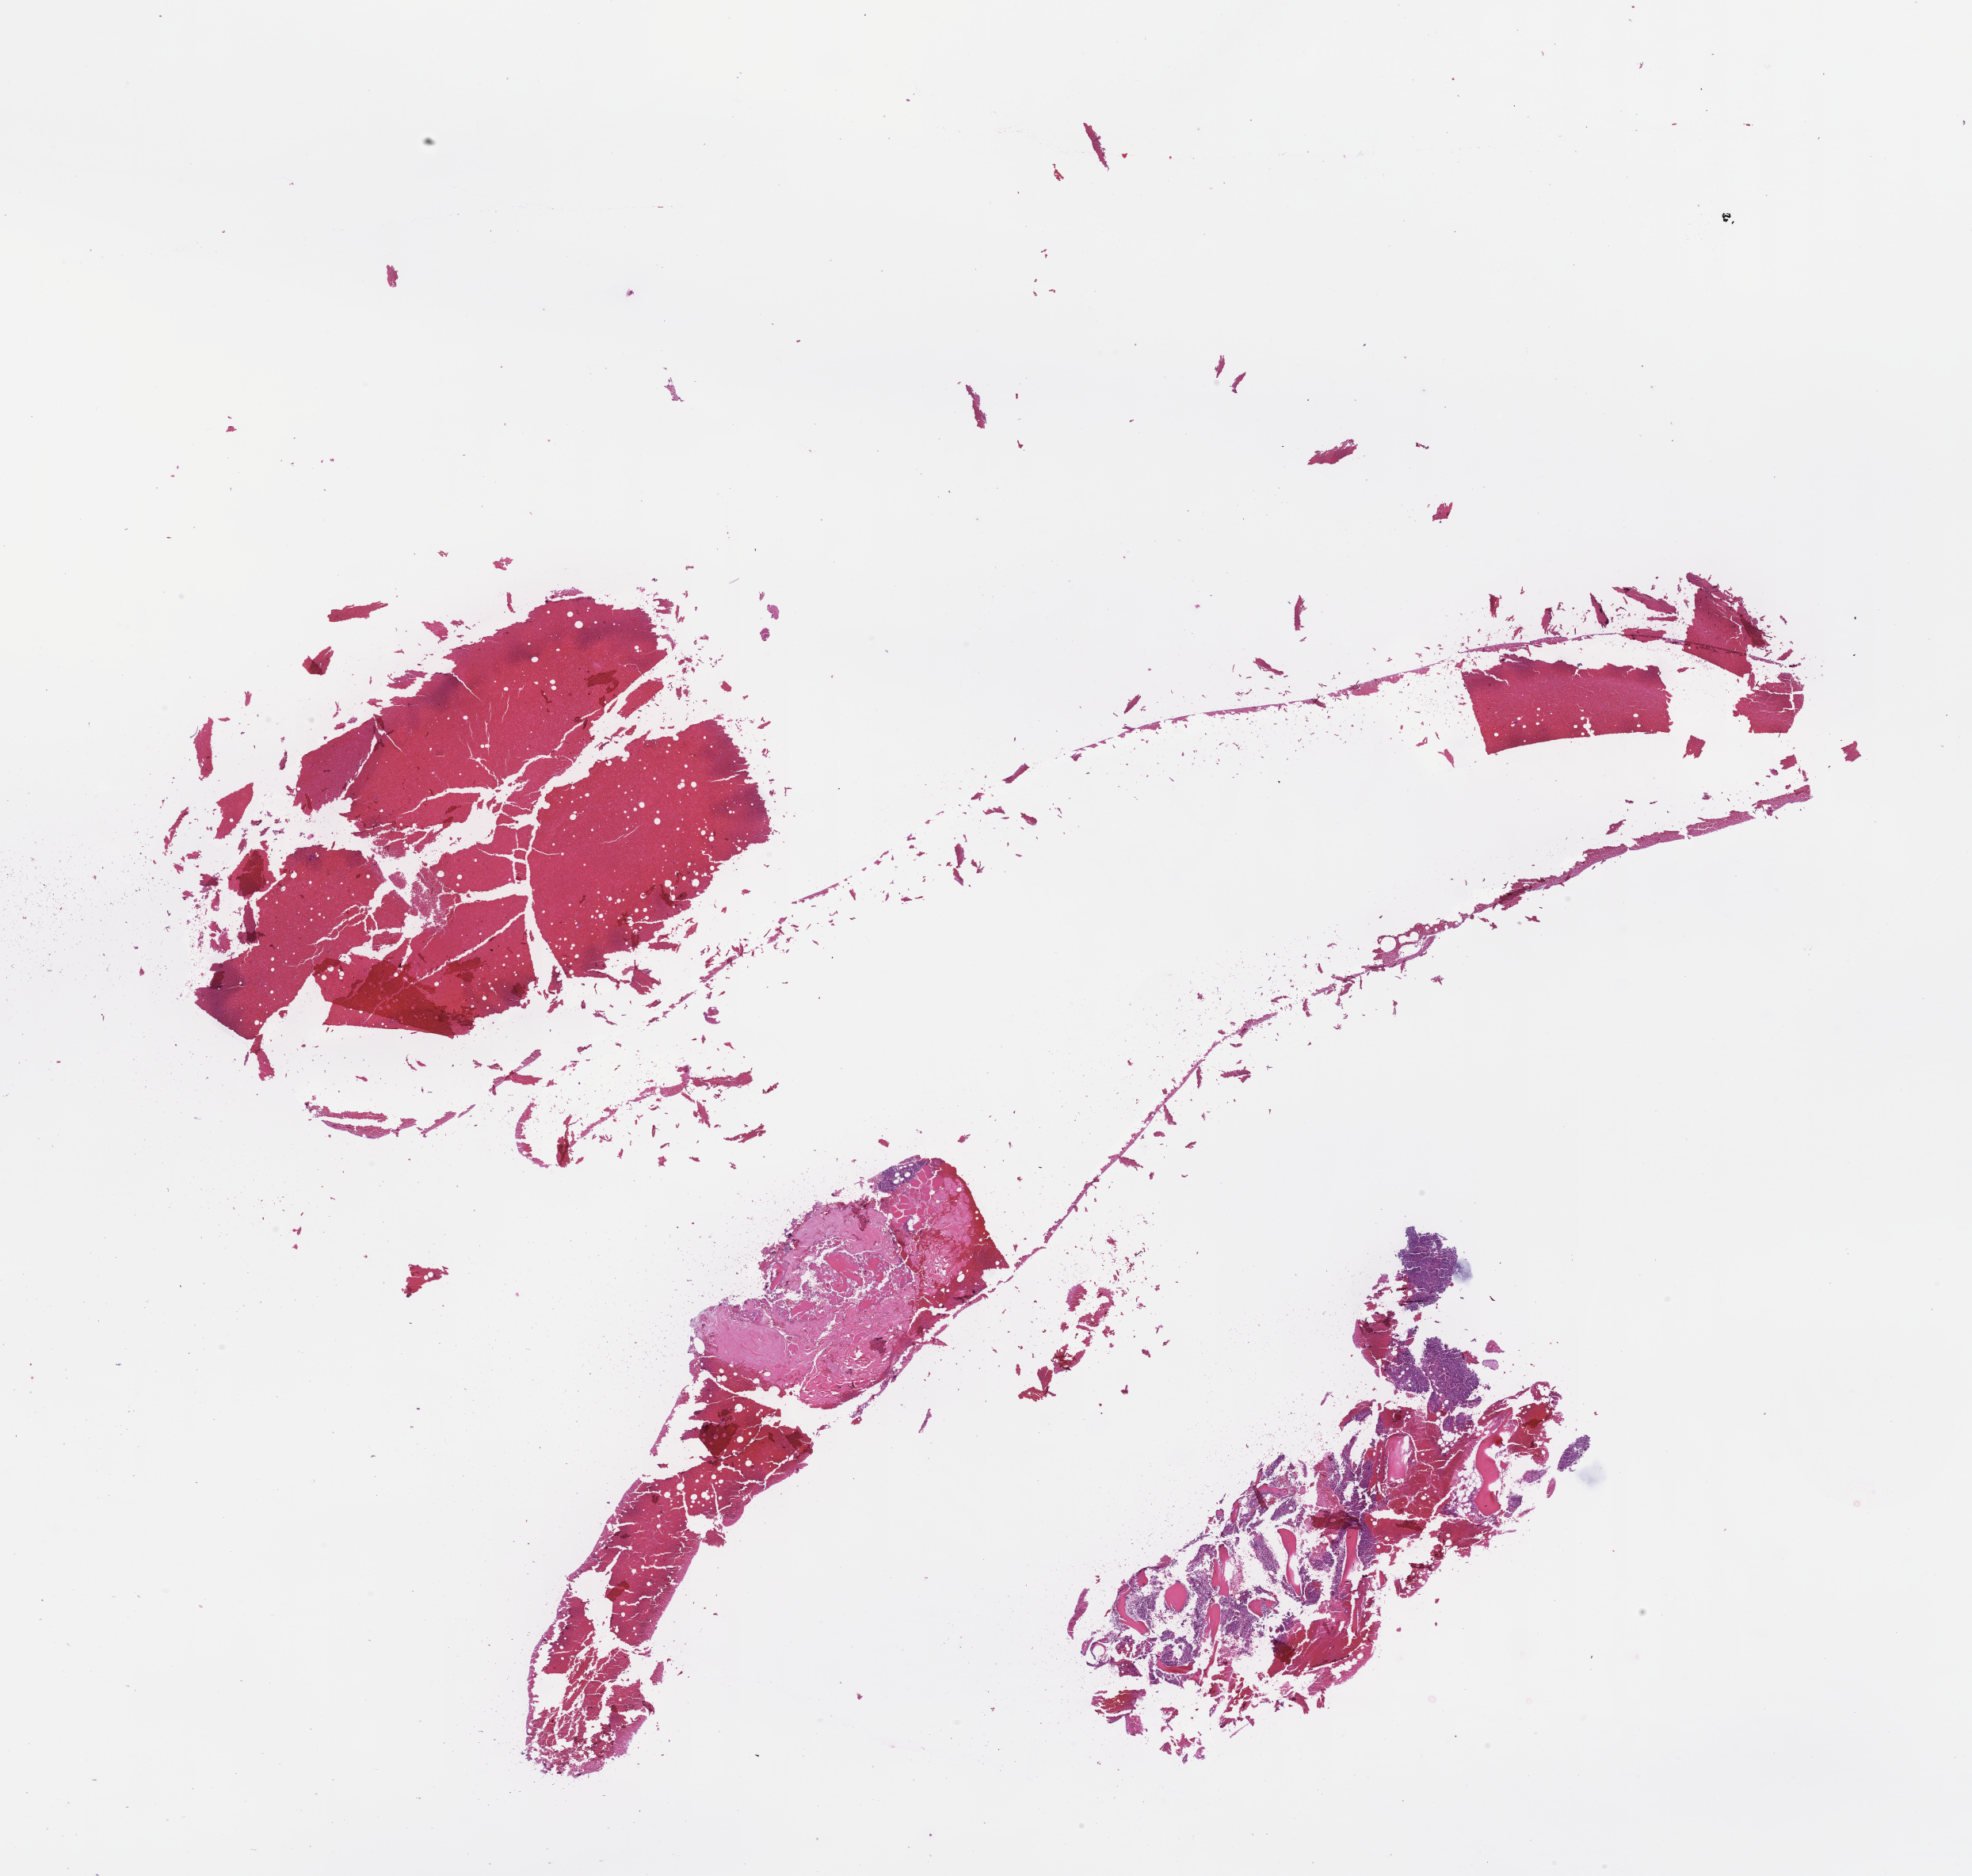
Whole-slide image, hematoxylin and eosin (H&E) stain — low-resolution overview of the scanned area, about 20.1 x 19.1 mm, formalin-fixed, paraffin-embedded (FFPE) tissue, site: bone marrow, specimen time point: archival tissue. Patient sex: male.
This section: primary tumour tissue. Diagnosis: Plasma Cell Myeloma.